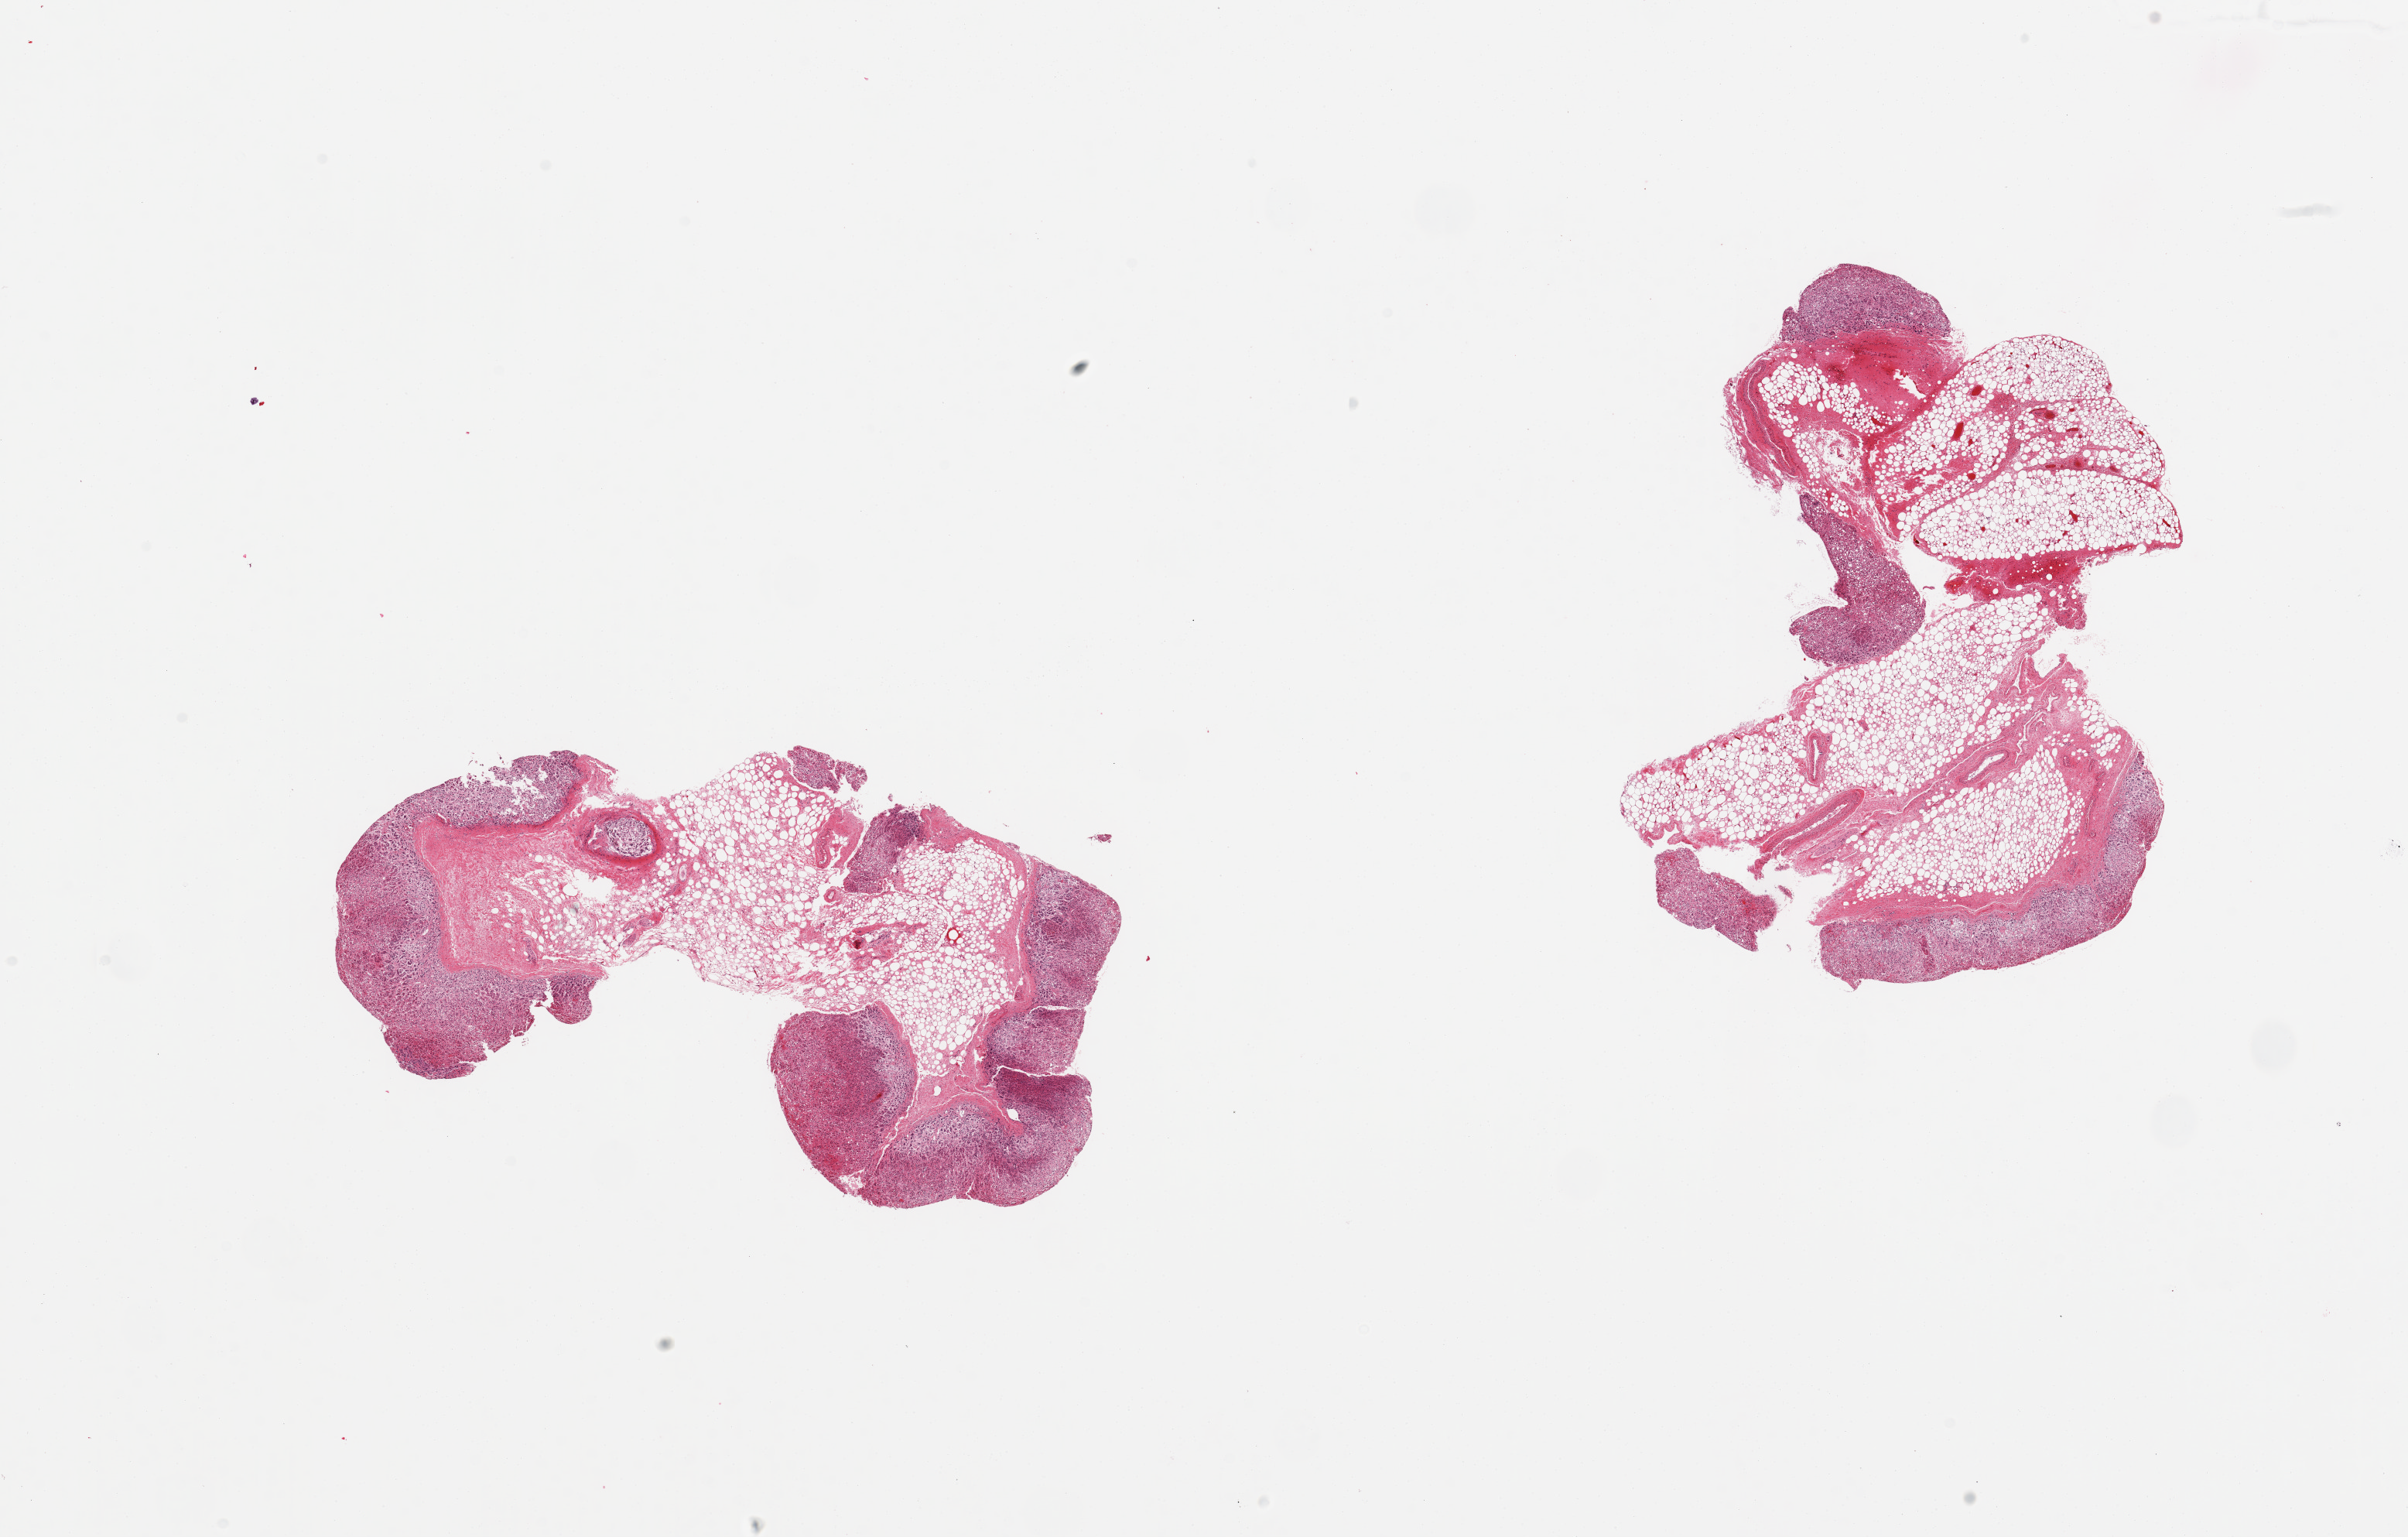
Haematoxylin and eosin whole-slide image, brightfield, whole scanned area (about 24.6 x 15.7 mm) shown as a low-resolution overview, PAXgene-fixed, paraffin-embedded tissue, section of adrenal gland (target tissue), donor tissue sample. Donor sex: male.
* pathologist's review note for this sample: 2 pieces, cortex, ~60% adherent/interstitial fat